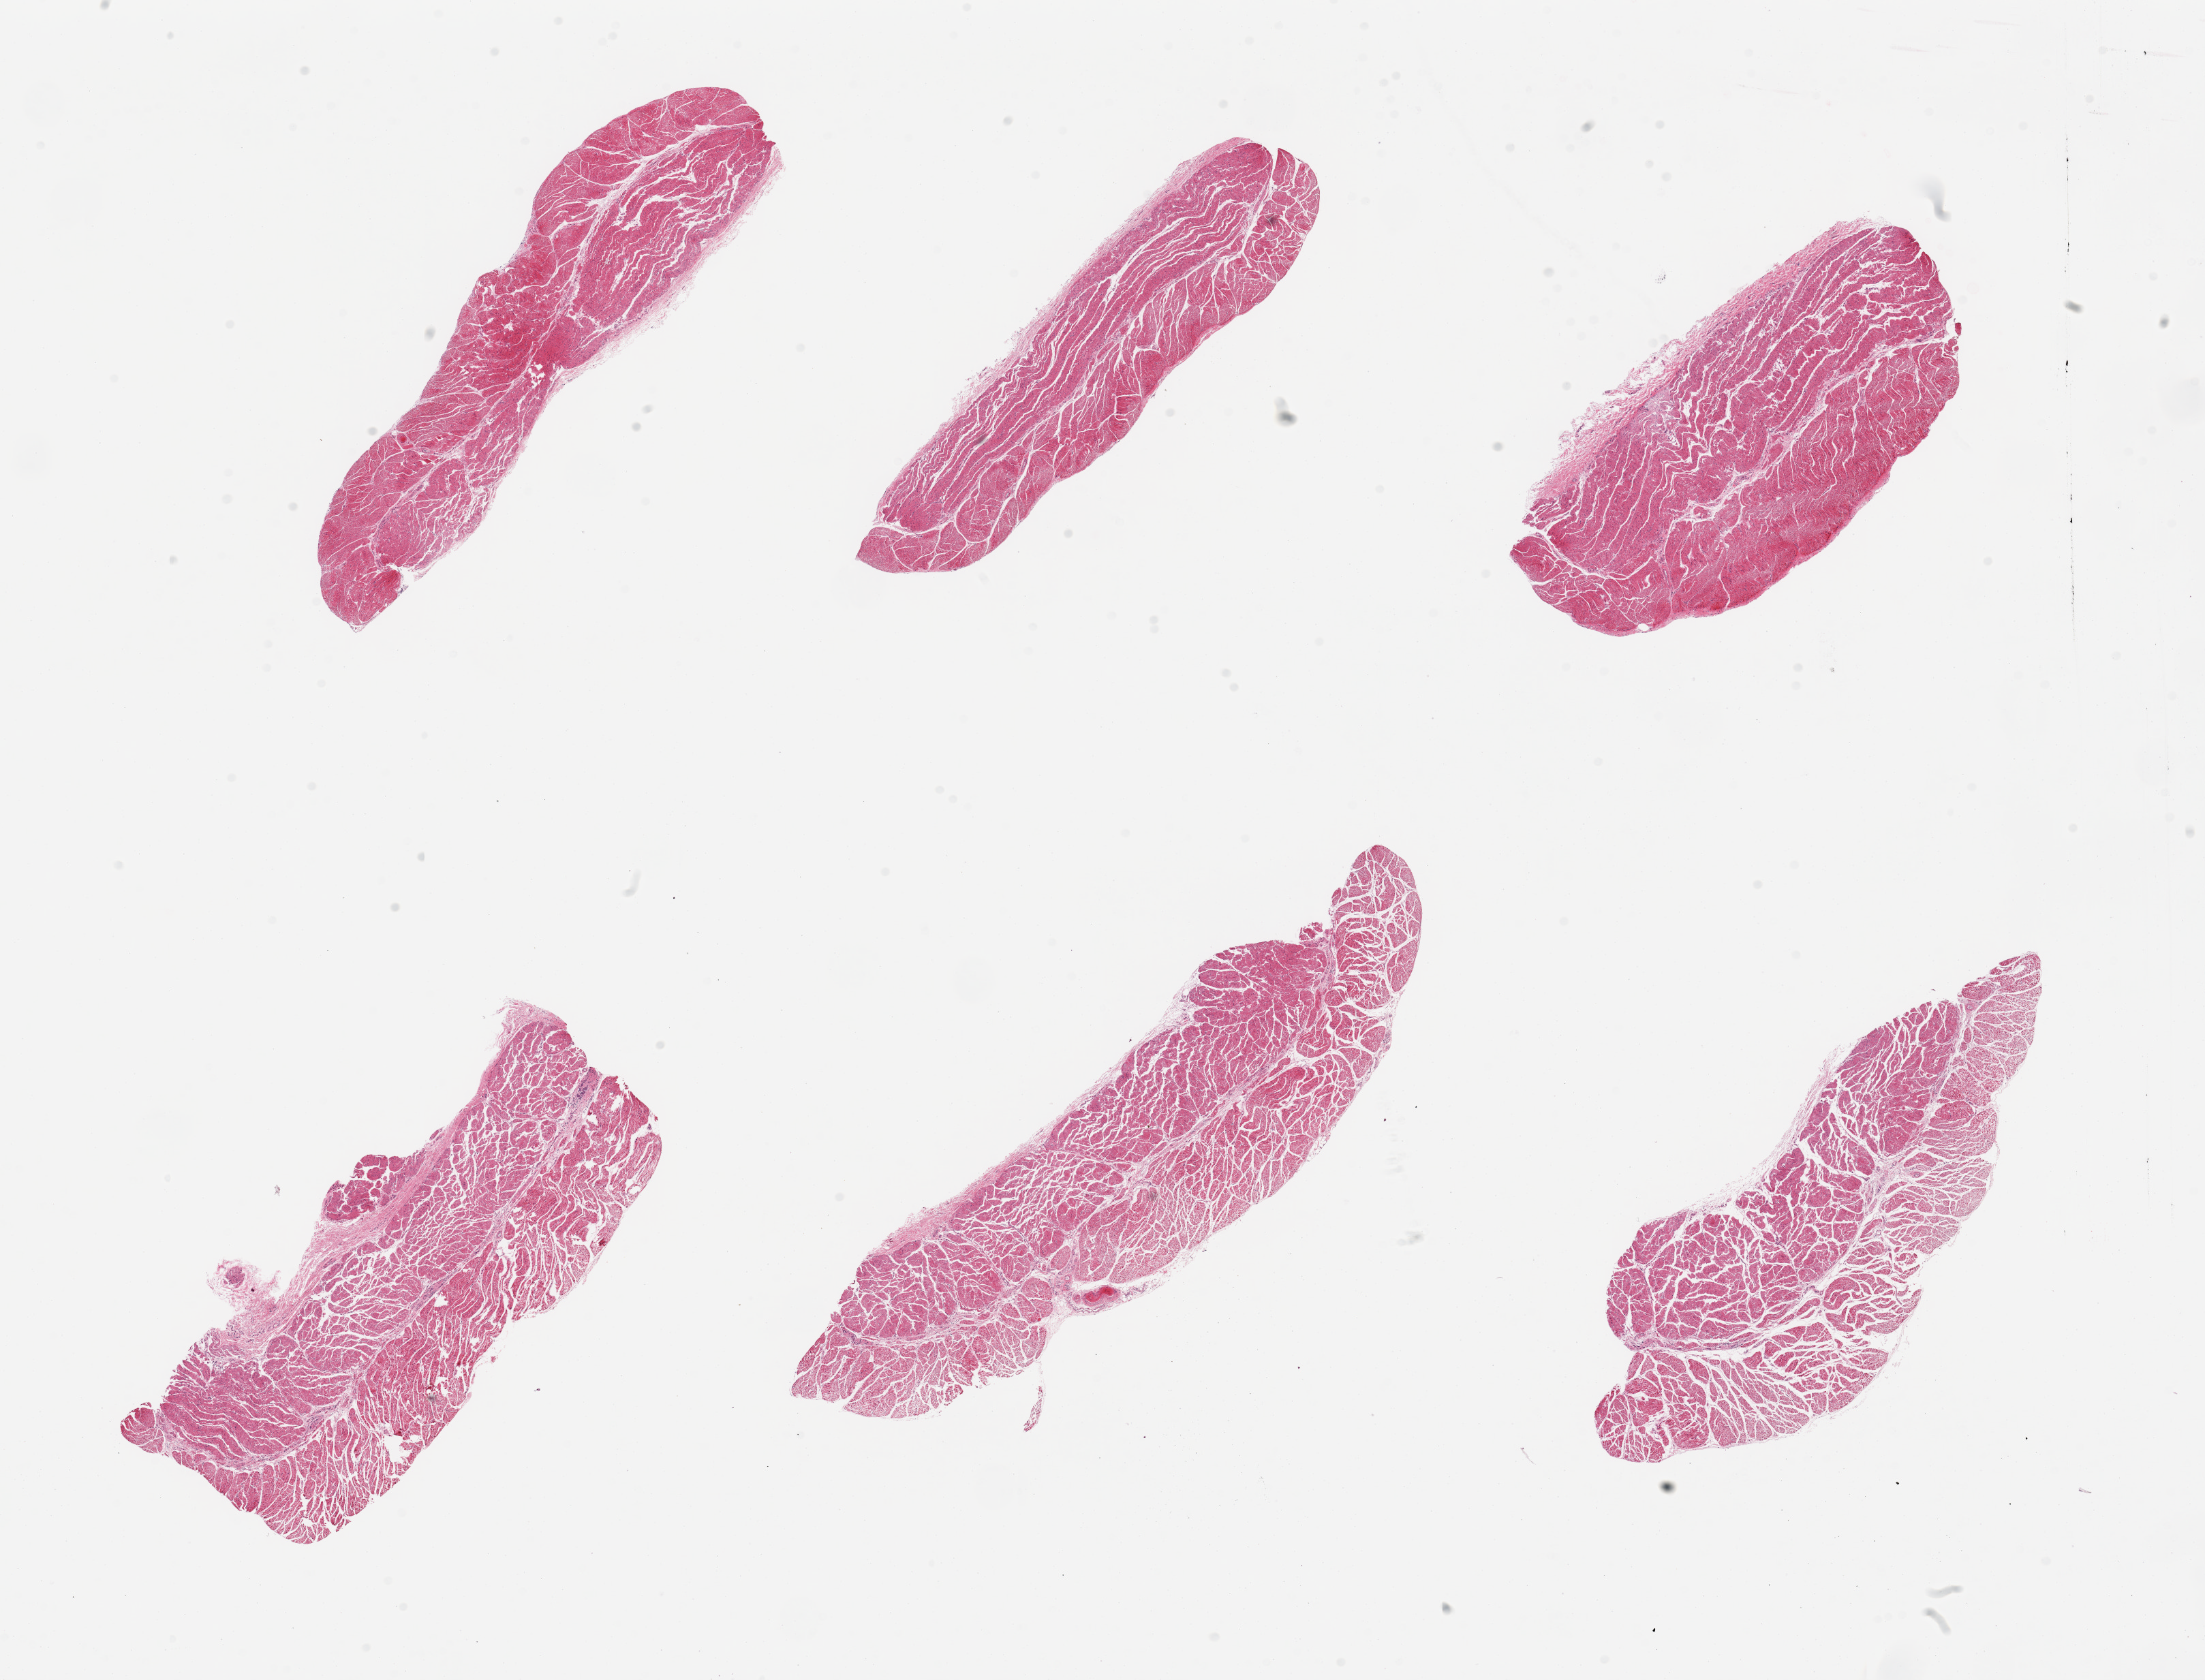
Haematoxylin and eosin whole-slide image — whole scanned area (about 25.6 x 19.5 mm, acquisition: 20x scan) shown as a low-resolution overview, PAXgene-fixed paraffin-embedded (PFPE) section, section of esophageal muscle (target tissue), tissue donor sample. Donor sex: male.
Reviewer comment on this tissue sample: 6 pieces, all target muscularis.